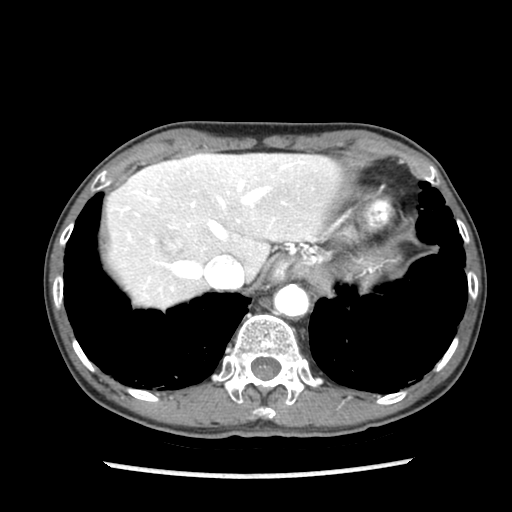
Contrast-enhanced abdominal CT (liver protocol), one axial slice. Position 68 of 87 along the scan axis. Reconstruction kernel STANDARD. 140 kVp. Soft-tissue window (W 400 / L 40 HU). 2.5 mm slice thickness. 512 × 512 image matrix, field of view 300 × 300 mm. From the clinical record (not read from this slice): diagnosis: hepatocellular carcinoma (patient treated with transarterial chemoembolisation; whether this scan precedes or follows treatment is not stated here); TNM stage (as recorded): Stage-IIIB; Child-Pugh class: A; tumour nodularity: uninodular.
Outlined on this slice (semi-automatically segmented with operator editing):
- liver parenchyma outside the tumour (the mass and vessels are separate outlines, so this box may not span the whole liver): box from (x=106, y=153) to (x=342, y=308) px
- mass: (x=159, y=230)–(x=185, y=255)
- liver vessels: (x=123, y=158)–(x=302, y=279)